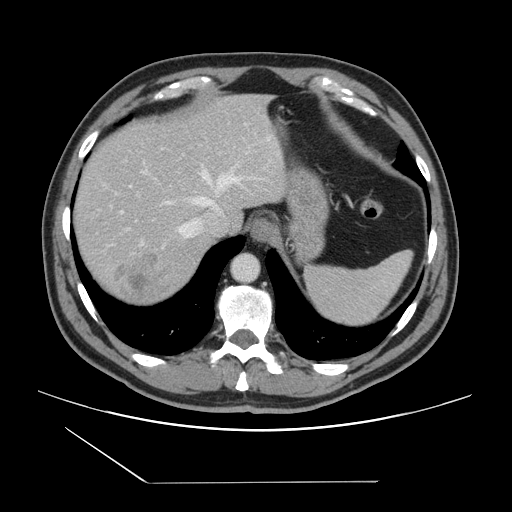
Contrast-enhanced abdominal CT, one axial slice. Slice 120 of 157 in the series (ordered by position). Intravenous contrast given. Soft-tissue window (W 400 / L 40 HU). 2.5 mm slice thickness. 512 × 512 image matrix. Male patient, age 61 years. Case-level facts recorded for this patient, not image findings: diagnosis: colorectal cancer liver metastases, imaged before liver resection.
Outlined on this slice (manually delineated by an expert):
- hepatic veins: bounding box (x1, y1, x2, y2) in pixels: (121, 152, 248, 248)
- liver: (73, 94, 286, 307)
- planned liver remnant (the part of the liver to remain after resection): (73, 96, 234, 231)
- portal vein (with intrahepatic branches): (128, 186, 131, 229)
- liver metastasis: (108, 253, 162, 305)